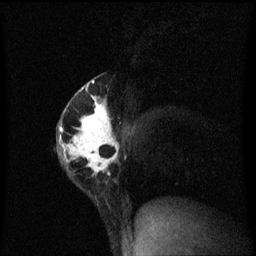
Breast MRI (dynamic contrast-enhanced), one sagittal slice; position 38 of 60 along the scan axis; dynamic contrast-enhanced series, image 2 of 3 at this slice position (ordered by acquisition); 1.5 T; TE 4.2 ms, TR 8.4 ms; 2 mm slice thickness; 256 × 256 image matrix, field of view 200 × 200 mm. Patient: female, 40 years.
Outlined on this slice (semi-automatic segmentation, software-assisted and operator-edited):
- analysis volume of interest (the breast-tissue region the enhancement analysis was run in; not a lesion): bounding box (x1, y1, x2, y2) in pixels: (58, 74, 120, 199)
- tumour enhancement mask (voxels above the 70 % enhancement threshold inside the analysis volume of interest): (60, 80, 120, 175)